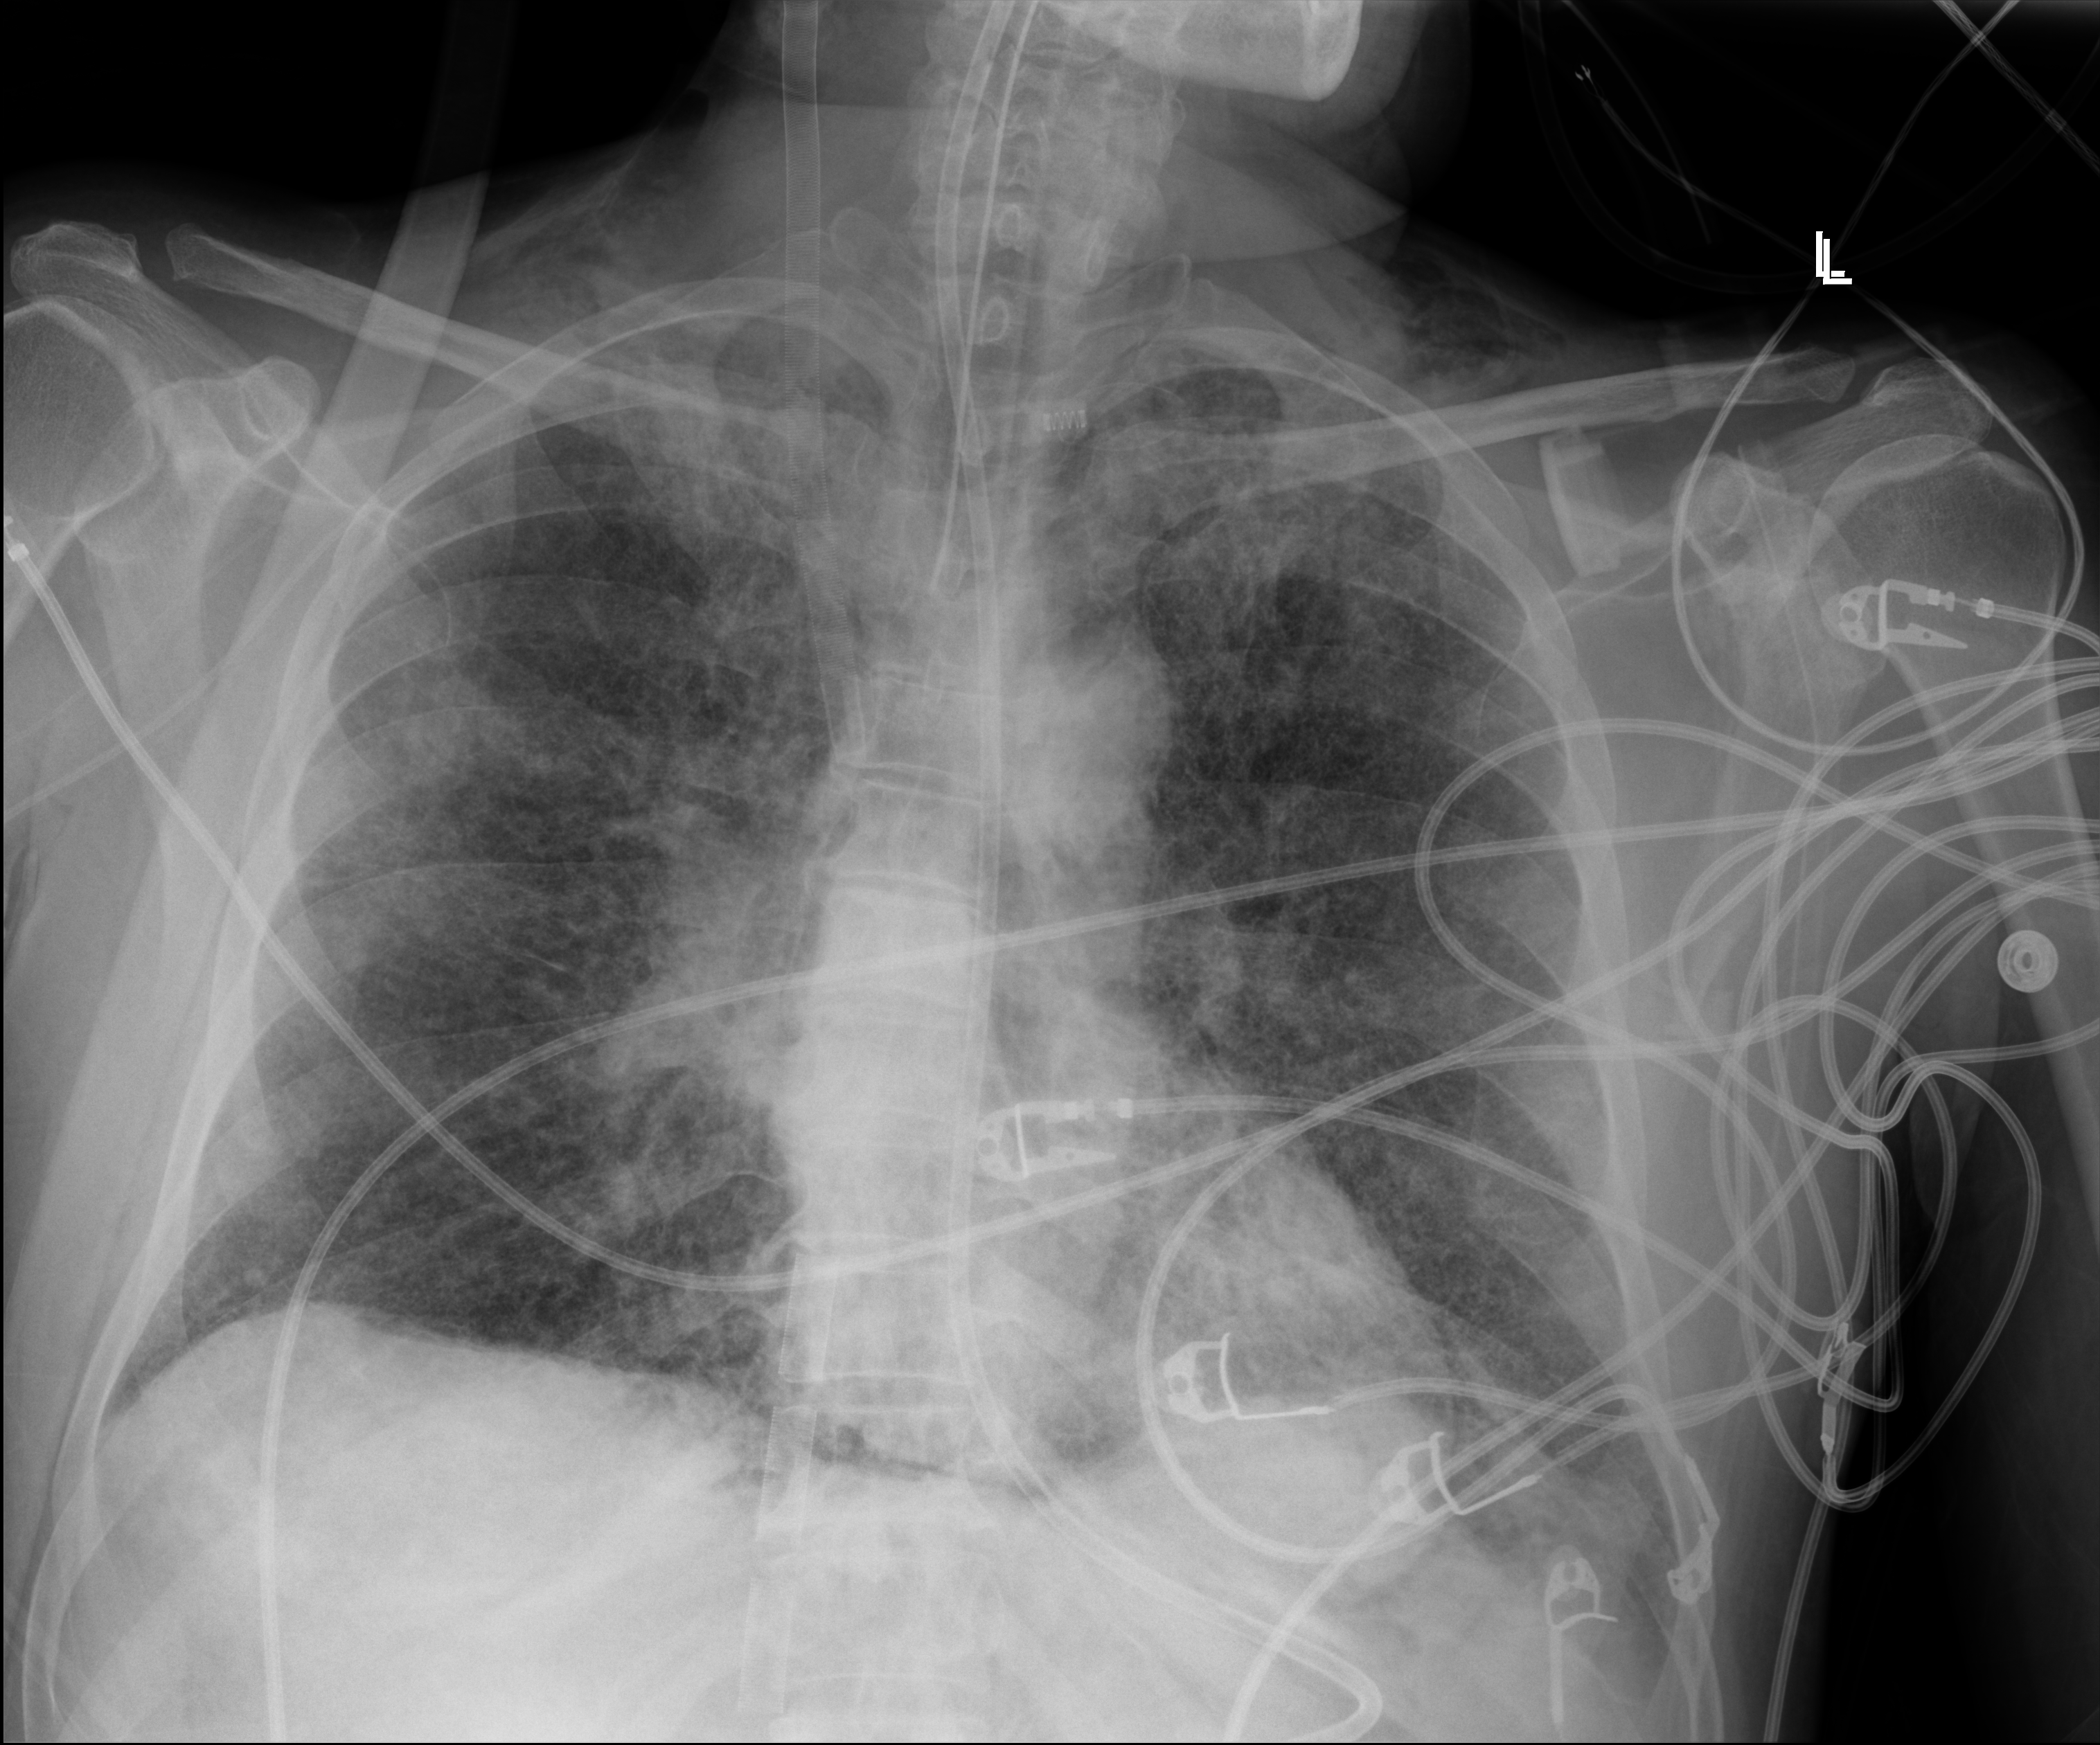
Chest radiograph (digital radiography). Patient hospitalised with COVID-19; male, aged 18–59 years.
Hospital-stay facts (about this admission, not read from this image; timing relative to this image not recorded): chronic kidney disease (admission record): no; mechanically ventilated during this hospital stay: yes; admitted to intensive care during this hospital stay: yes.